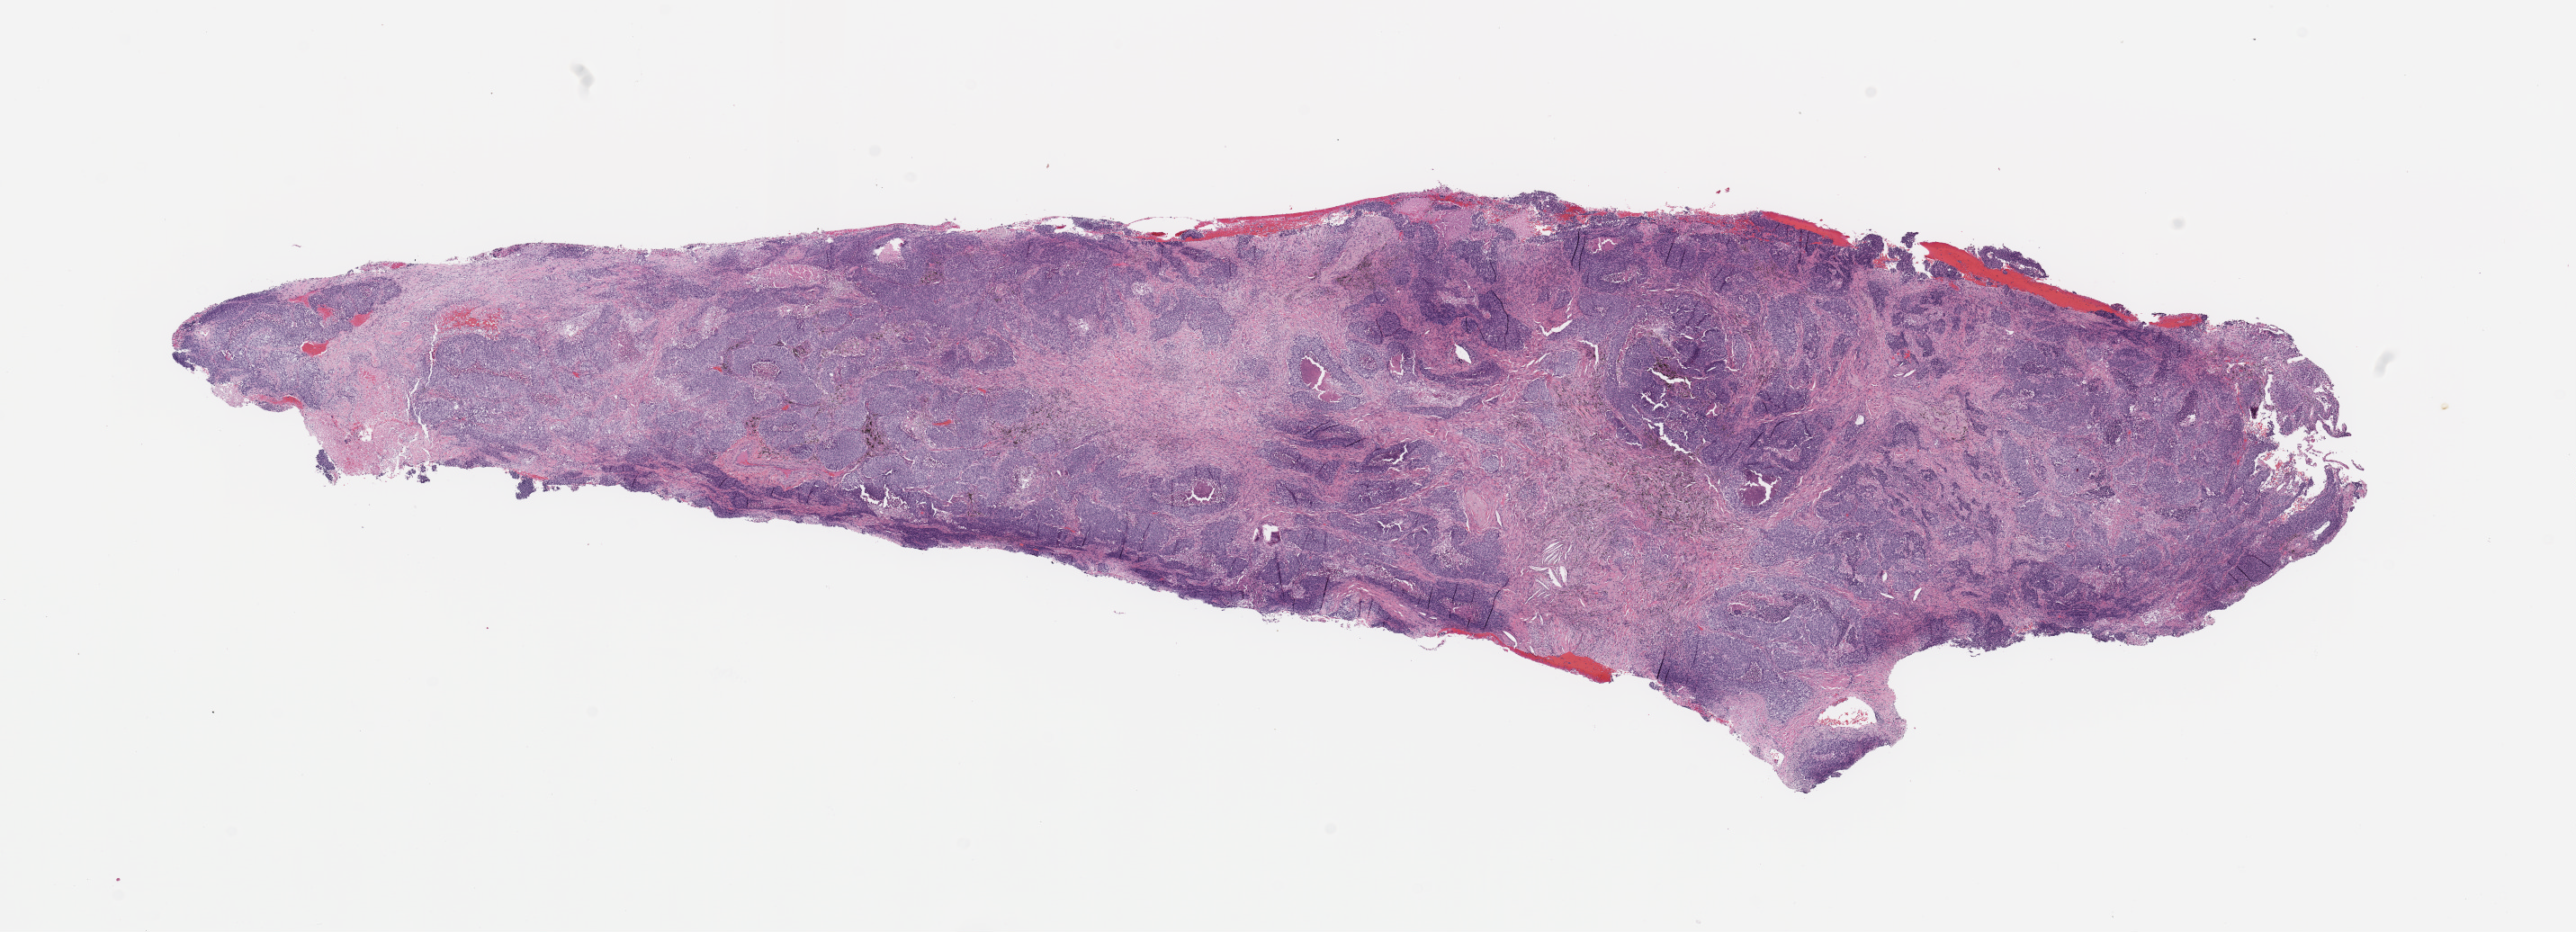
Whole-slide histology image, H&E, shown as a low-resolution overview of the whole scanned area (about 22.6 x 8.2 mm, from a 20x scan); tumour tissue sample, sampled site: lung. Patient: male, age 59 years. Histologic grade: G3 (poorly differentiated). Composition of this section per pathologist review: tumour nuclei 70%, necrosis 7%.
Diagnosis: Squamous cell carcinoma, NOS. Primary tumour site (as recorded): right upper lobe. AJCC pathologic stage: IB.